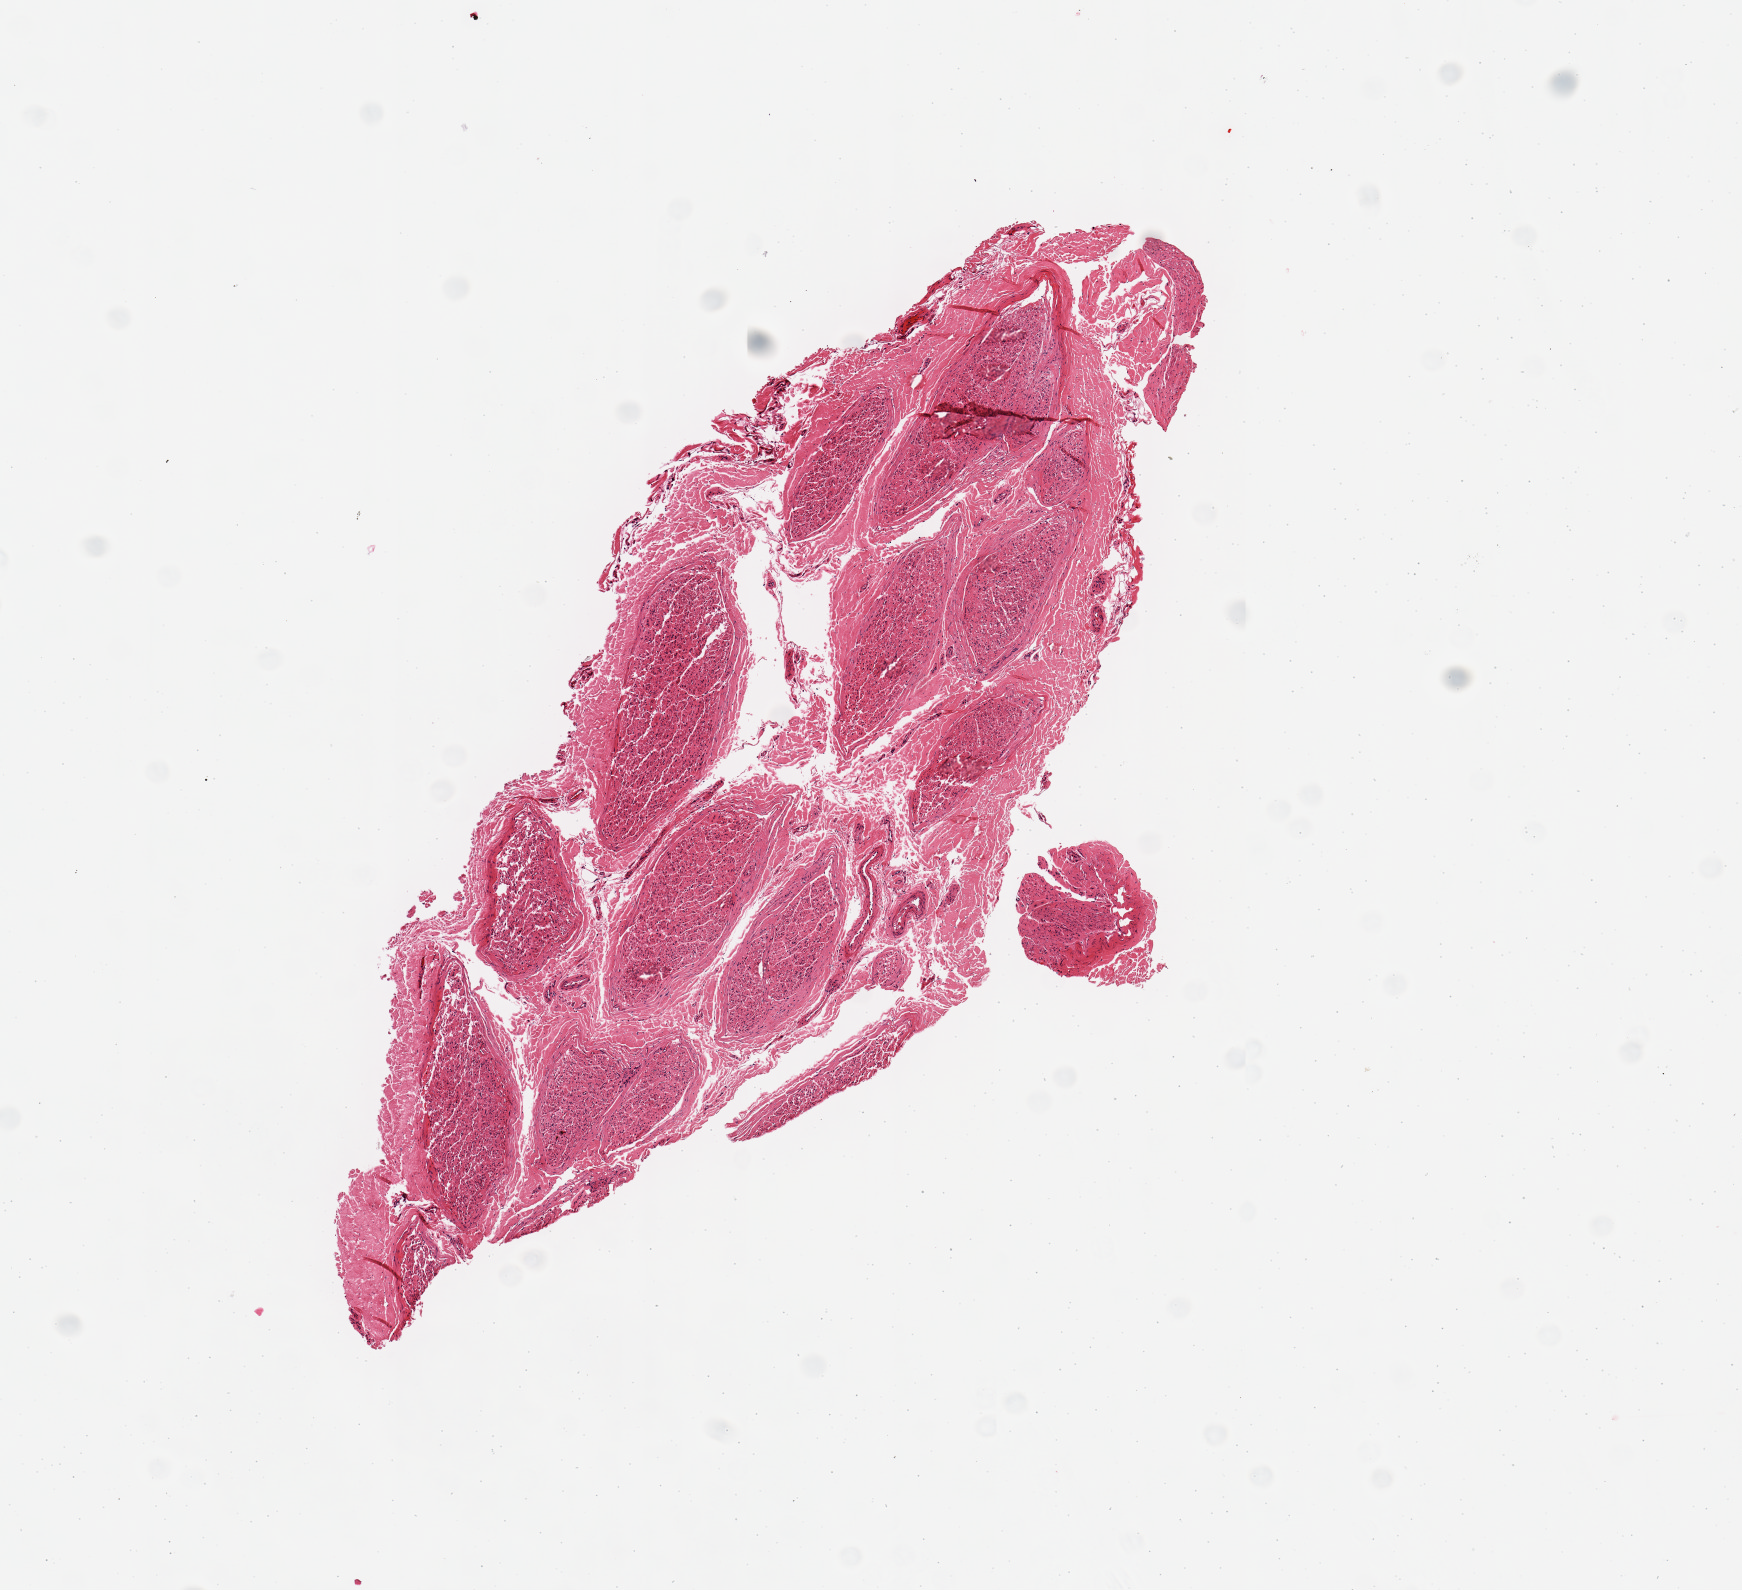
Whole-slide image, H&E stain — whole scanned area (about 6.9 x 6.3 mm) shown as a low-resolution overview, PAXgene-fixed paraffin-embedded (PFPE) section, target tissue: tibial nerve, tissue donor sample. Male donor.
- pathologist's review note for this sample: 1 piece; nerve NOT artery